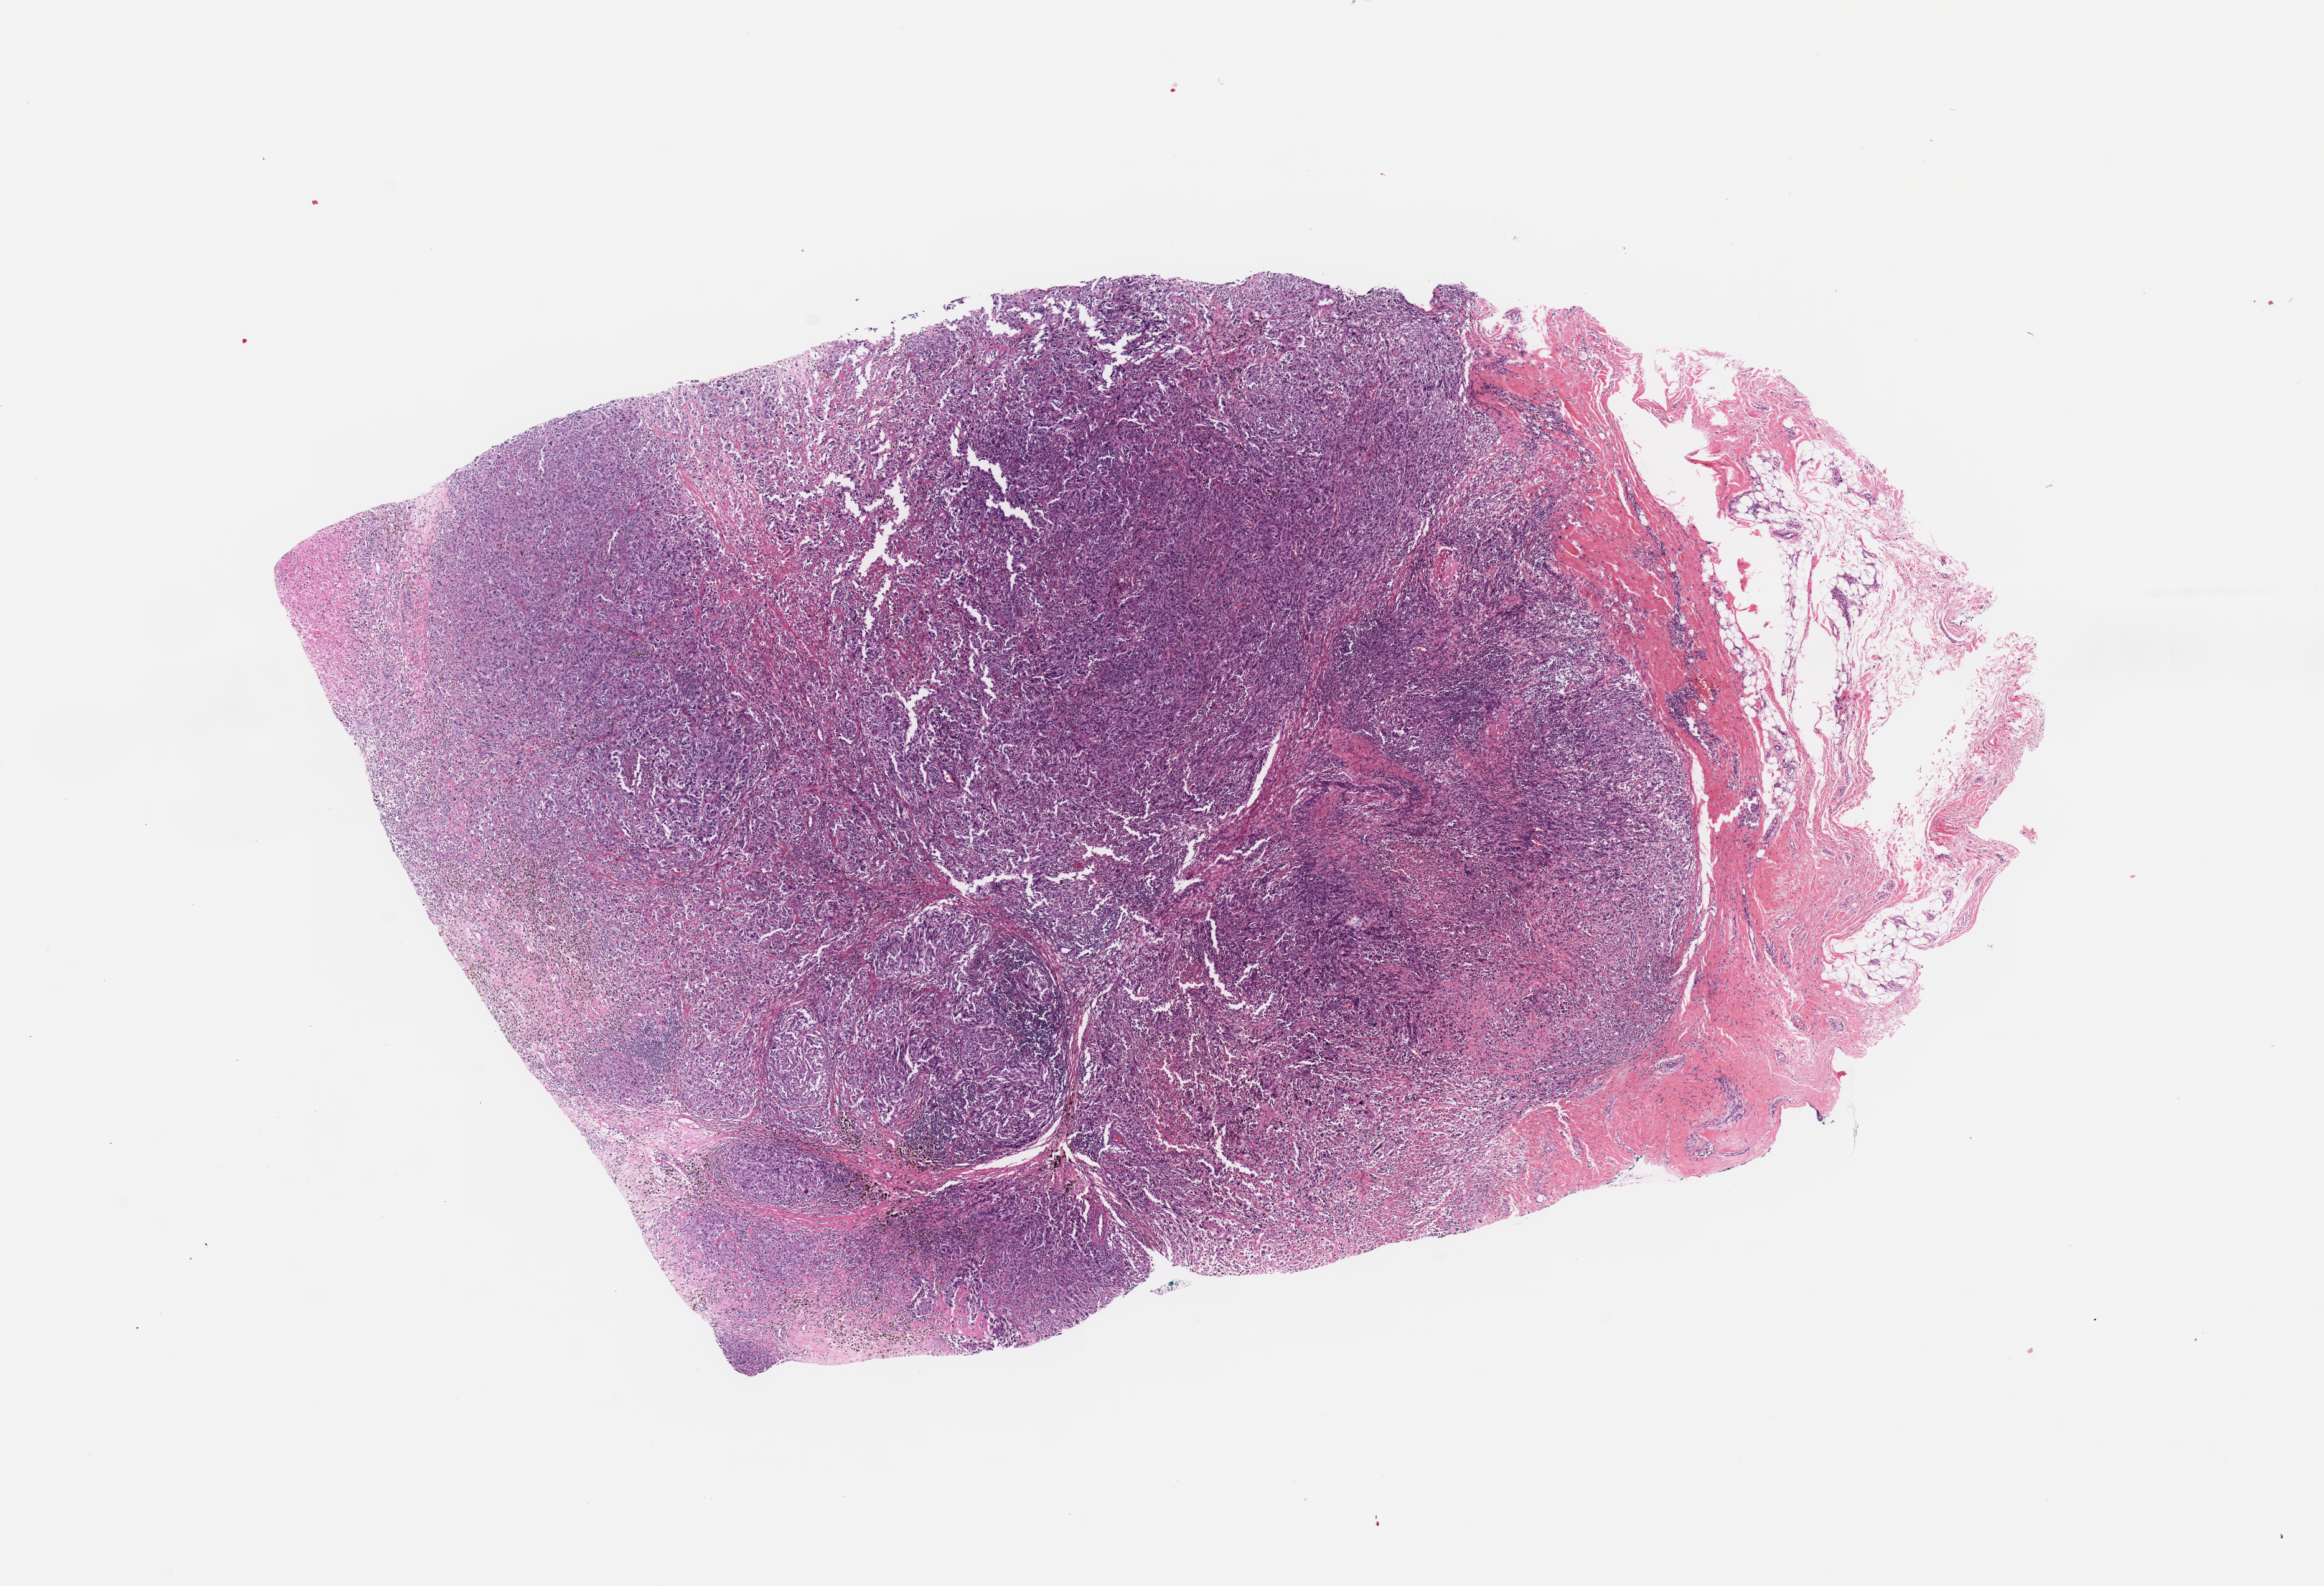
Hematoxylin and eosin (H&E) stained whole-slide image, a low-resolution overview of the entire scanned area, about 14.8 x 10.1 mm; melanoma tumour tissue; sampled site not recorded. Male, 83 y/o.
AJCC pathologic stage: IV. Primary tumour site (as recorded): trunk. Histologic diagnosis: Malignant melanoma, NOS.